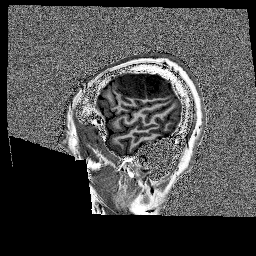
Brain MRI from a brain-tumour surgery series, one sagittal slice; slice 32 of 176 in the series (ordered by position); 1 mm slice thickness; 256 × 256 image matrix, field of view 256 × 256 mm. Case-level facts recorded for this patient, not image findings: histopathology: Glioblastoma; WHO grade: 4; IDH mutation: no; tumour location: Left Frontal.
Outlined on this slice (expert manual segmentation):
- tumour: bounding box (x1, y1, x2, y2) in pixels: (118, 73, 175, 99)